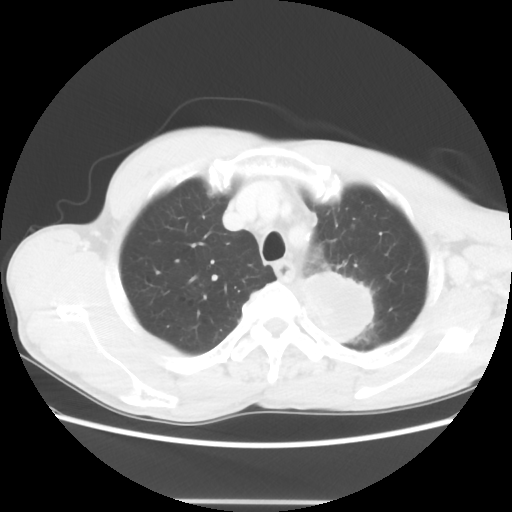
Chest CT, one axial slice; position 53 of 62 along the scan axis; 100 kVp; lung window (W 1500 / L -600 HU); 5 mm slice thickness; 512 × 512 image matrix, field of view 360 × 360 mm. Male patient, age 61 years. Case-level facts recorded for this patient, not image findings: clinical TNM (as recorded): T3 N1 M1.
Outlined on this slice (rectangle marked by the reading radiologist):
- lung tumour (recorded histology: adenocarcinoma): bounding box <293,261,379,355> (left, top, right, bottom; pixels)